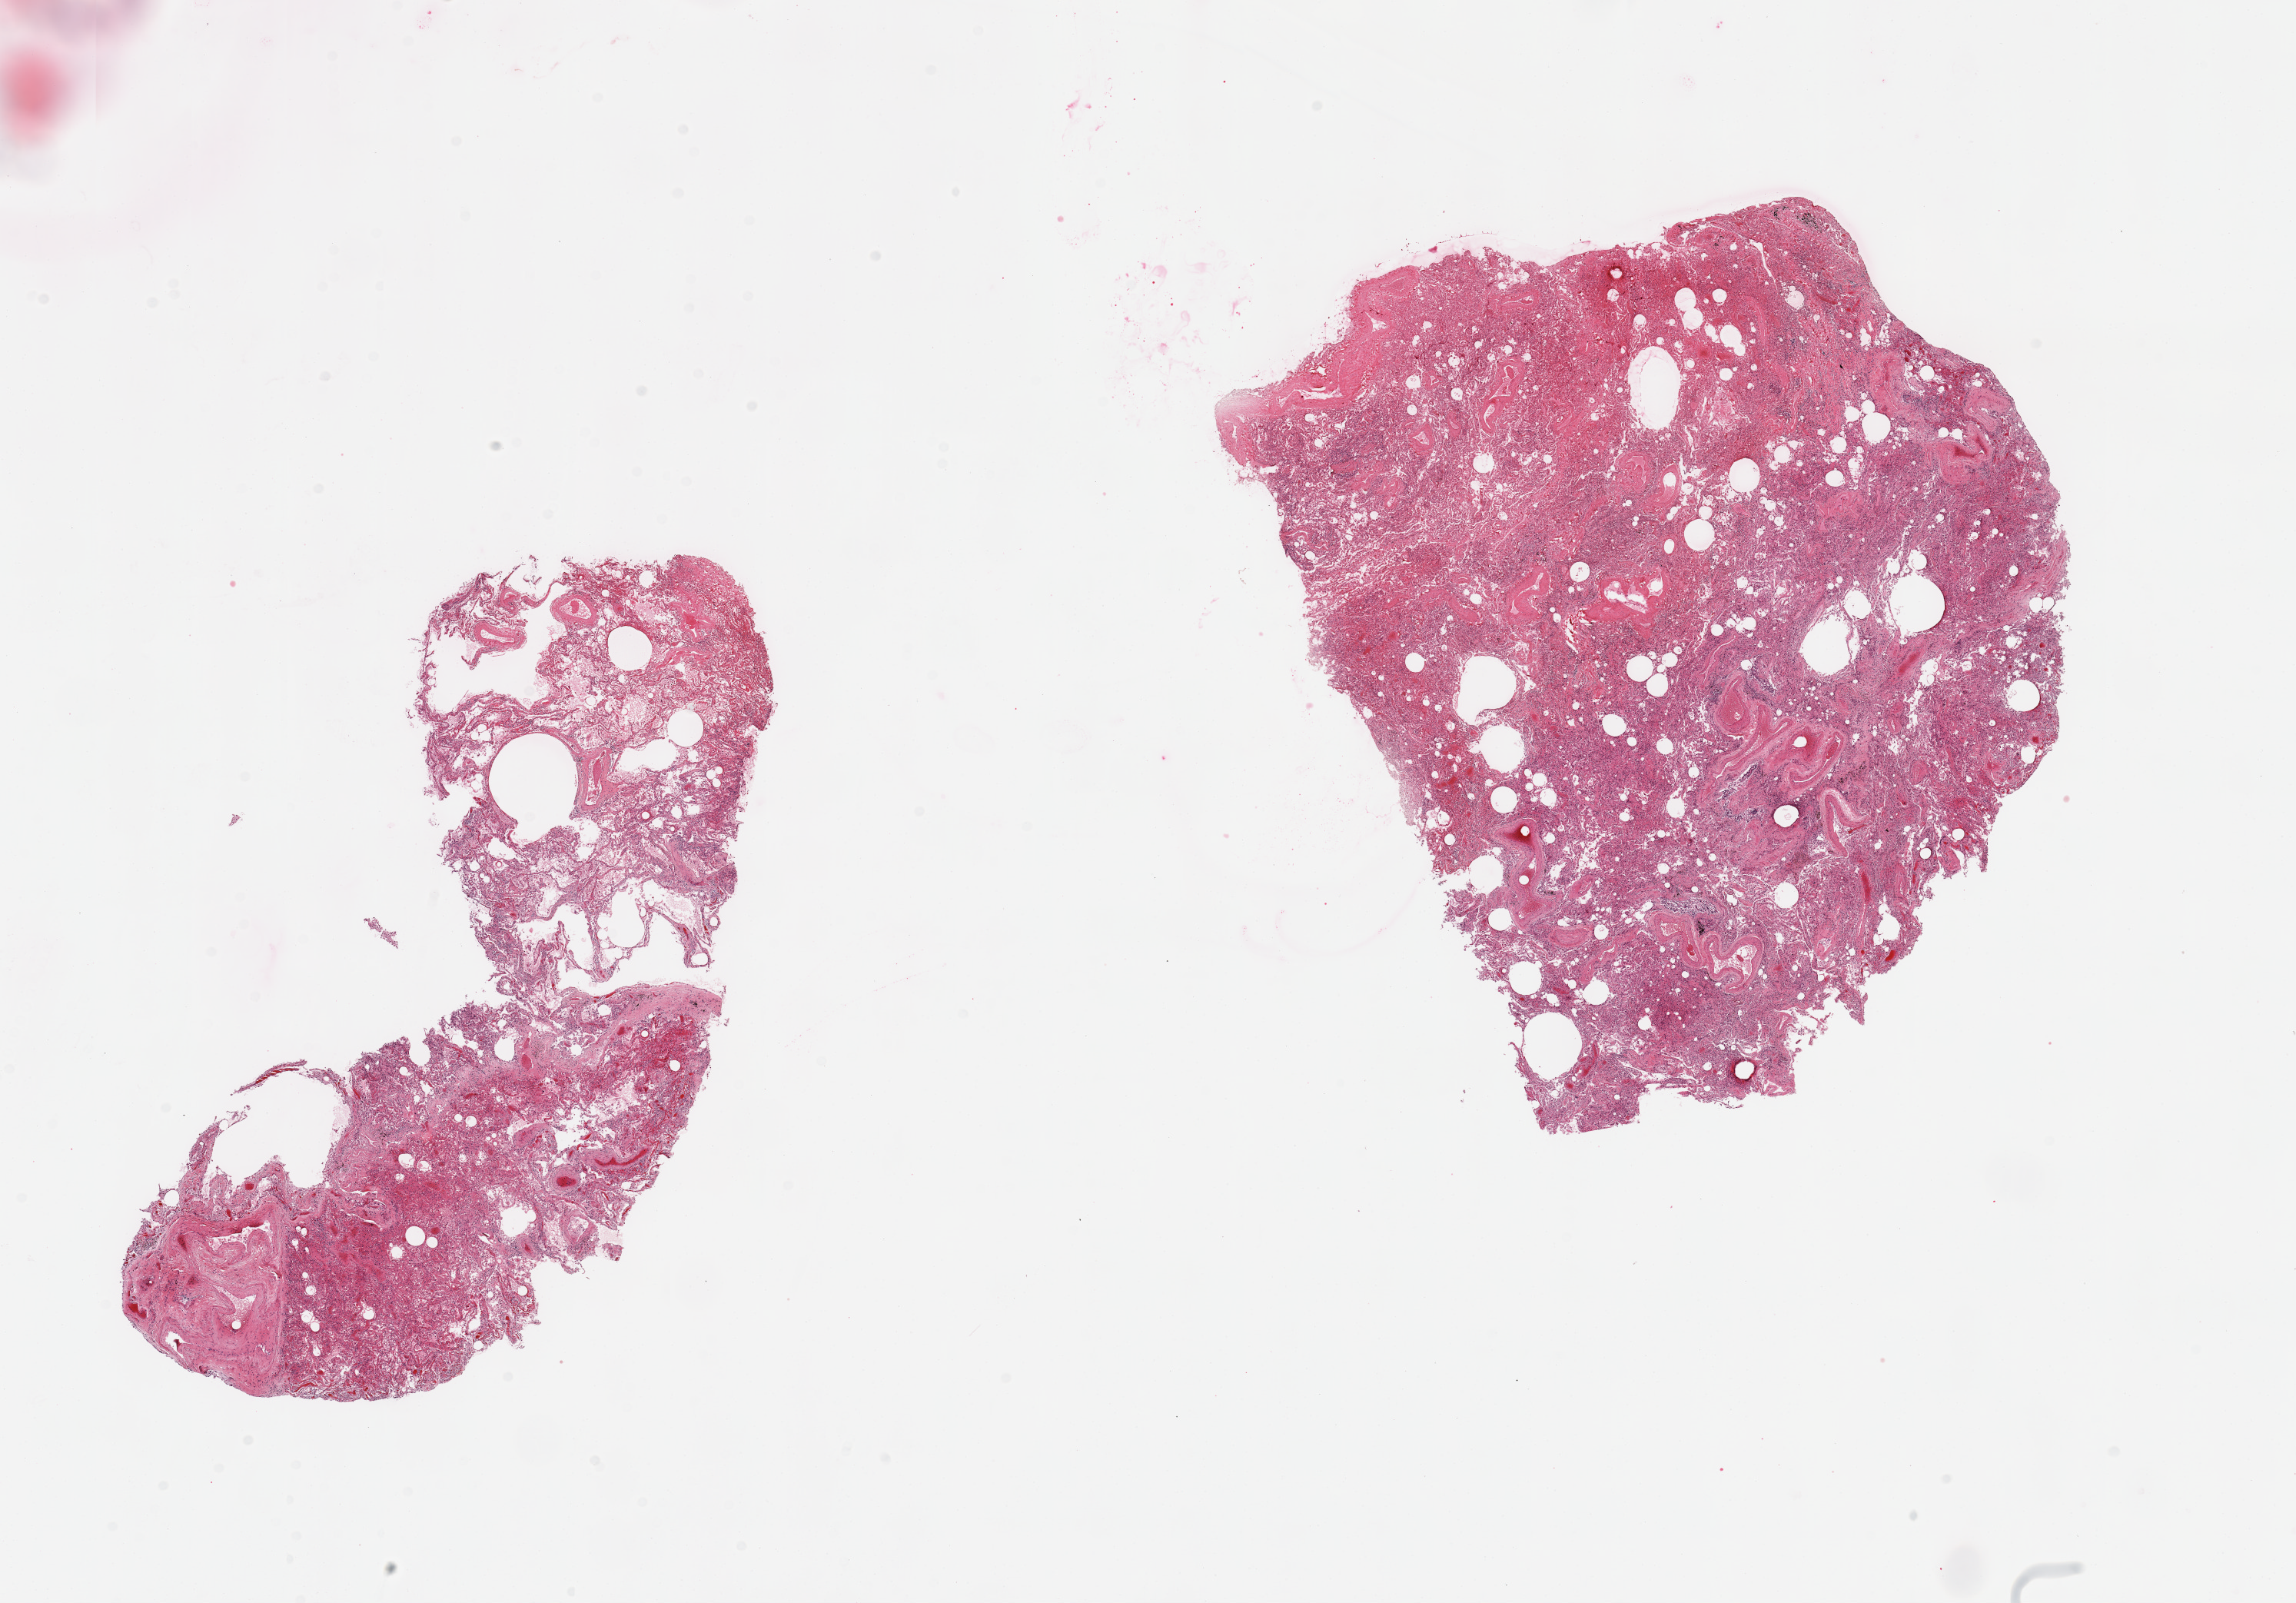
Digitized haematoxylin and eosin-stained section — whole scanned area (about 23.6 x 16.5 mm) shown as a low-resolution overview, PAXgene-fixed, paraffin-embedded tissue, section of lung (target tissue), donor tissue sample. Donor: male.
Reviewer comment on this tissue sample: 2 pieces; emphysema and atelectasis (alveolar collapse), congestion; thick walled vessels.